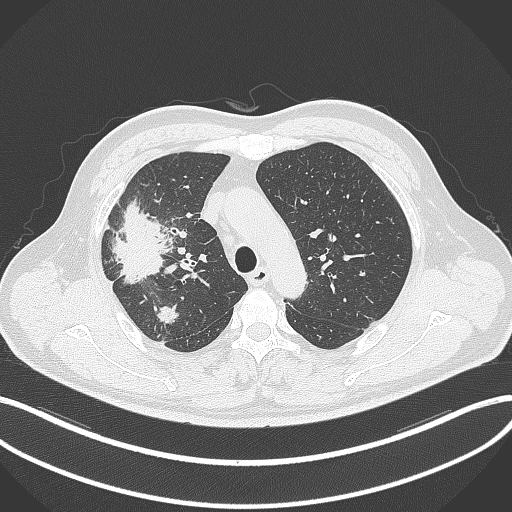
Chest CT, one axial slice. Reconstruction kernel B70f. 120 kVp. Lung window (W 1500 / L -600 HU). 1 mm slice thickness. 512 × 512 image matrix, field of view 400 × 400 mm. Patient: male, 55 years. From the clinical record (not read from this slice): clinical TNM (as recorded): T3 N2 M1.
Annotated regions visible in this slice (rectangle marked by the reading radiologist):
- lung tumour (recorded histology: adenocarcinoma): bounding box <109,195,168,286> (left, top, right, bottom; pixels)